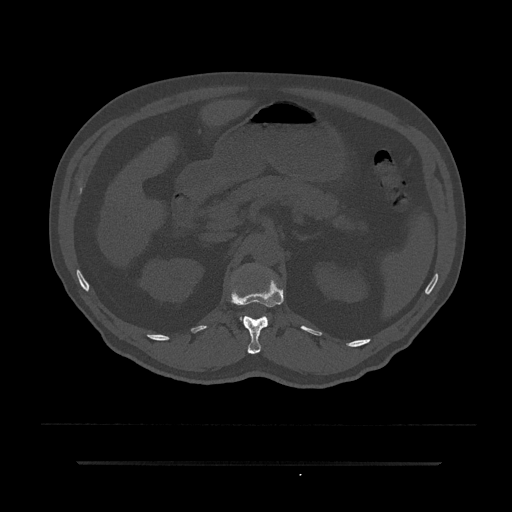
CT including the spine, one axial slice; position 187 of 797 along the scan axis; reconstruction kernel Br40s/3; 120 kVp; bone window (W 1800 / L 400 HU); 512 × 512 image matrix, field of view 464 × 464 mm. Male patient, age 59 years. Case-level facts recorded for this patient, not image findings: primary cancer: bile ducts; vertebrae with lytic lesions (as recorded): T10.
Structures marked on this image (semi-automatically segmented with operator editing):
- L1 vertebra: bounding box [x1, y1, x2, y2] px = [243, 316, 268, 319]
- T12 vertebra: [229, 276, 284, 354]